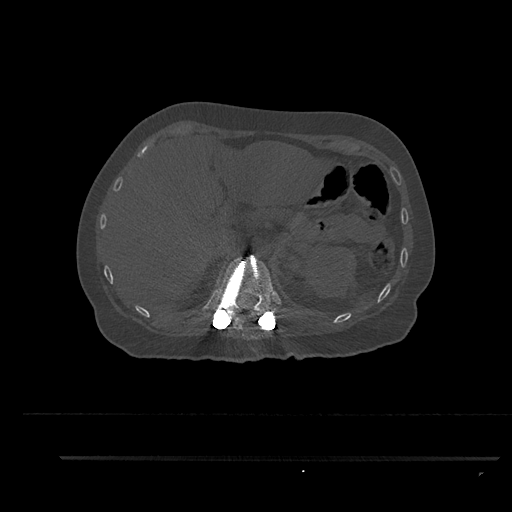
CT including the spine, one axial slice; slice 278 of 797 in the series (ordered by position); 120 kVp; bone window (W 1800 / L 400 HU); 512 × 512 image matrix, field of view 408 × 408 mm. Female patient, age 44 years. From the clinical record (not read from this slice): primary cancer: renal; vertebrae with lytic lesions (as recorded): L1.
Annotated regions visible in this slice (semi-automatically segmented with operator editing):
- T11 vertebra: bounding box <233,317,253,341> (left, top, right, bottom; pixels)
- T12 vertebra: <213,256,282,319>